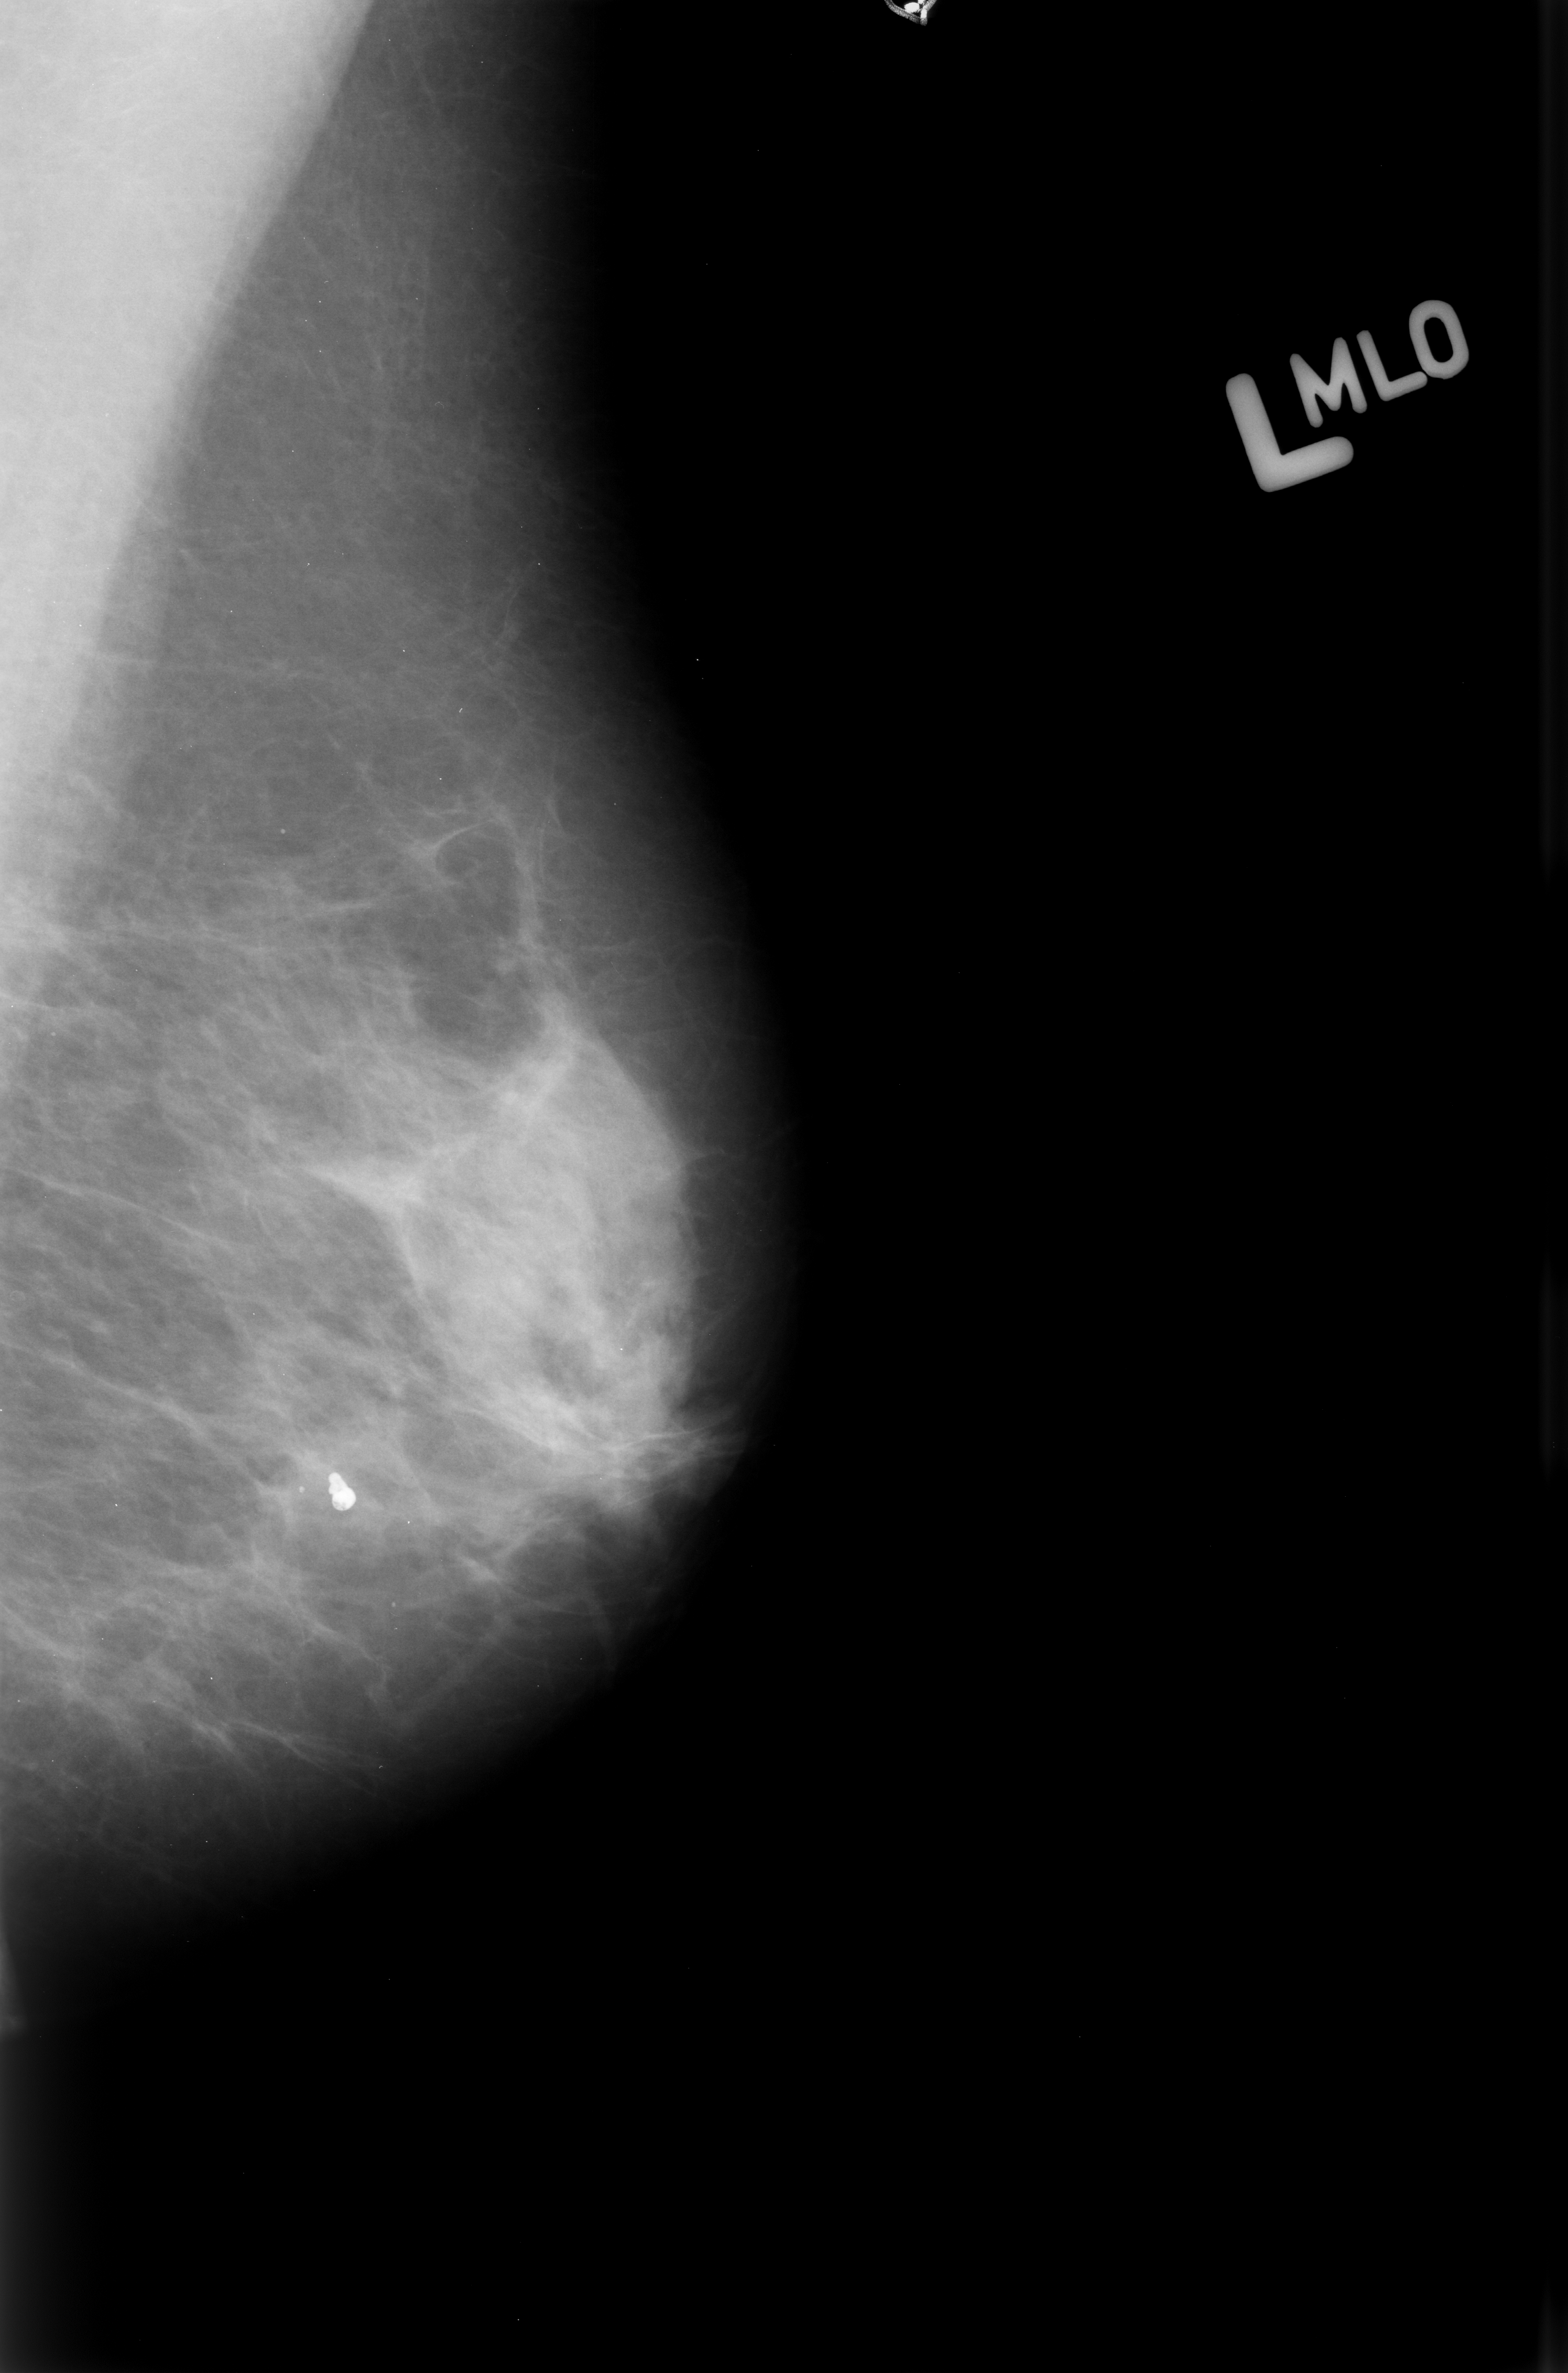
Scanned film-screen mammogram; left breast; mediolateral oblique (MLO) view; breast composition: heterogeneously dense (BI-RADS density category 3 of 4); 1568 × 2373 image matrix.
Marked abnormalities (boxes around the expert regions of interest):
- calcifications, morphology coarse; BI-RADS assessment category 2; outcome (as recorded, no biopsy): benign without callback (not worked up further): bounding box [x1, y1, x2, y2] px = [293, 1442, 399, 1552]